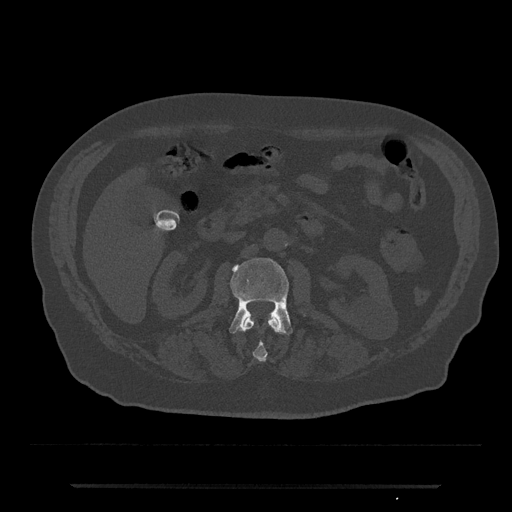
CT including the spine, one axial slice. Position 493 of 797 along the scan axis. Reconstruction kernel Br40s/3. Bone window (W 1800 / L 400 HU). 512 × 512 image matrix. Patient: male, 80 years. From the clinical record (not read from this slice): primary cancer: prostate; vertebrae with lytic lesions (as recorded): L1, T11.
Annotated regions visible in this slice (semi-automatic segmentation, software-assisted and operator-edited):
- L1 vertebra: bounding box [x1, y1, x2, y2] px = [242, 316, 281, 361]
- L2 vertebra: [229, 258, 293, 335]